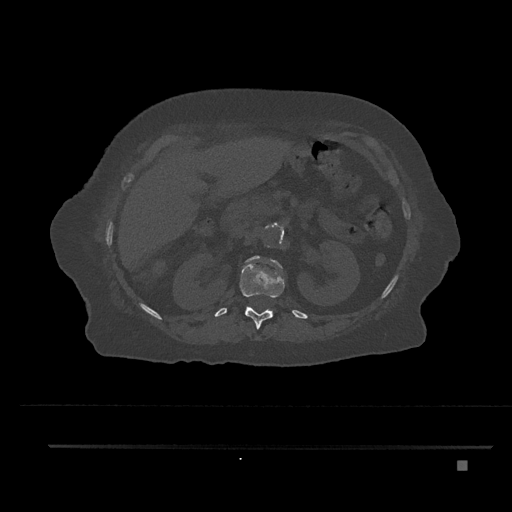
CT including the spine, one axial slice; 120 kVp; bone window (W 1800 / L 400 HU); 512 × 512 image matrix. Female patient, age 76 years. Case-level facts recorded for this patient, not image findings: primary cancer: lung; vertebrae with lytic lesions (as recorded): T11, L3.
Structures marked on this image (semi-automatically segmented with operator editing):
- L1 vertebra: box from (x=246, y=256) to (x=284, y=278) px
- T12 vertebra: (x=236, y=262)–(x=285, y=329)